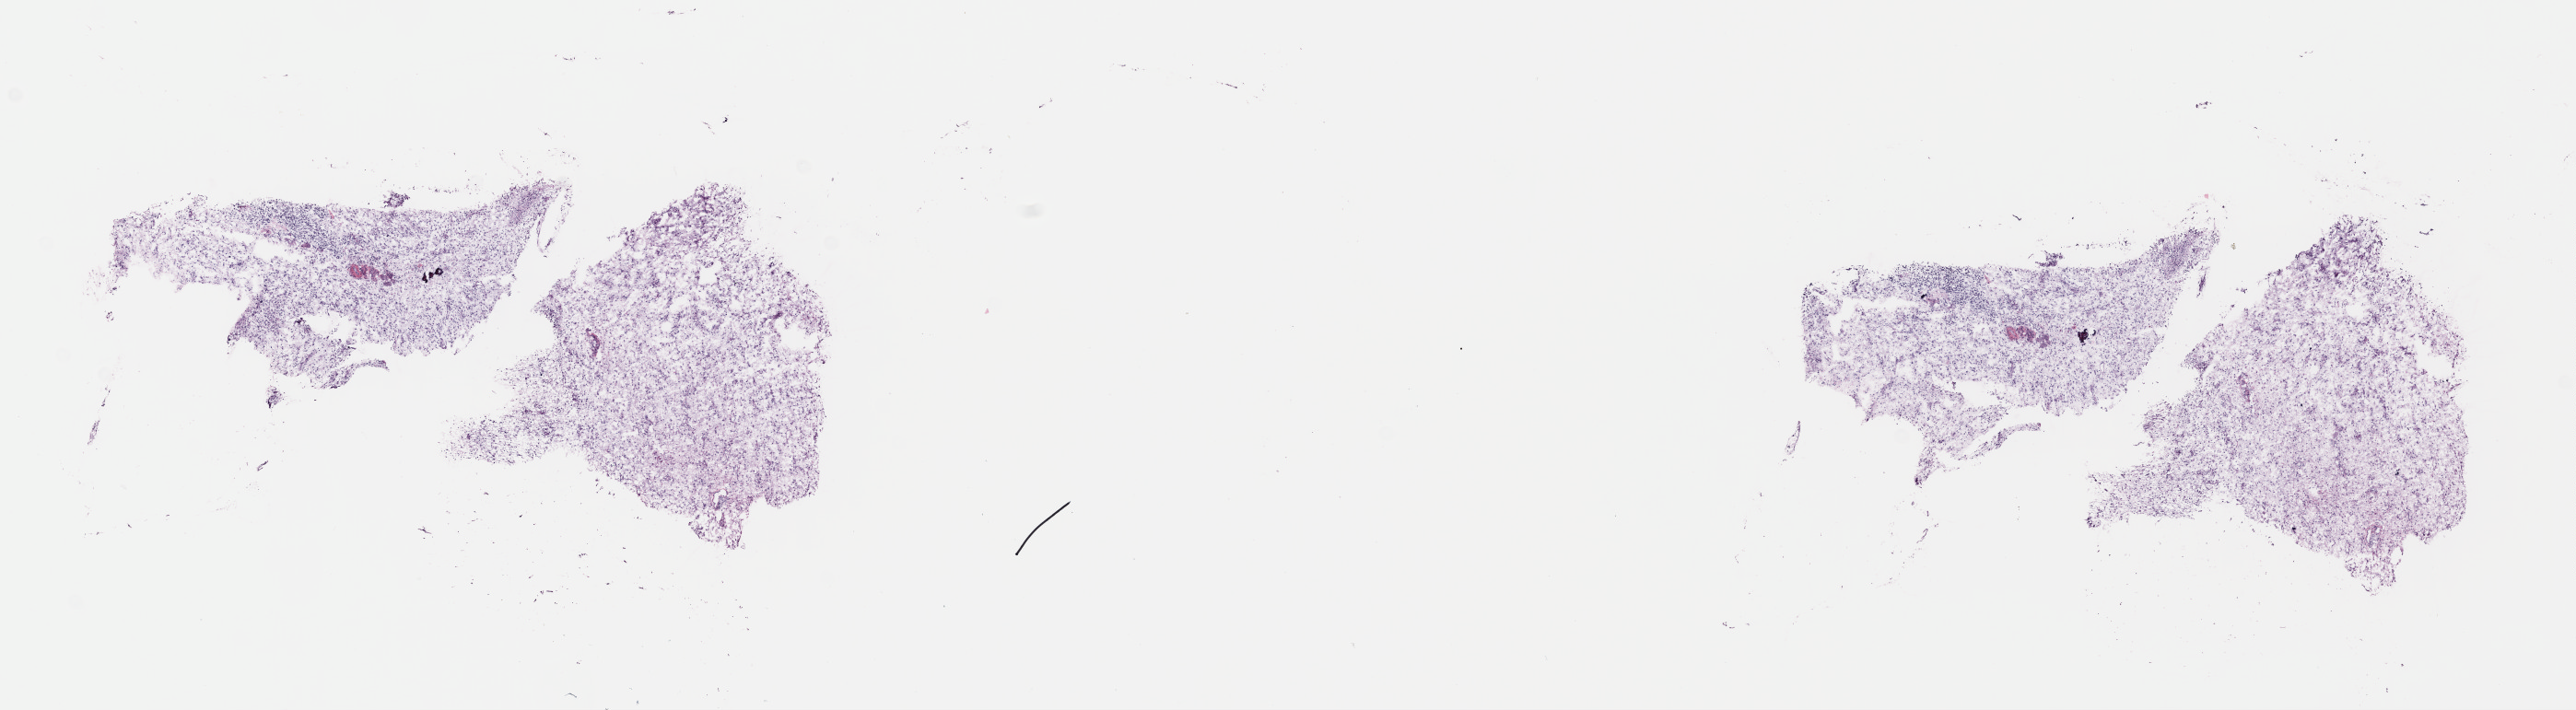
Whole-slide histology image, H&E-stained — low-resolution overview of the scanned area, about 22.0 x 6.1 mm (acquisition: 40x scan); frozen section from the top of the tissue portion; sample: primary tumour, brain. Female, age 39 years at initial diagnosis. Histologic grade: G2 (moderately differentiated). Composition of this section per pathologist review: tumour cells 40%, tumour nuclei 80%, normal cells 10%, stromal cells 50%, necrosis 0%. Infiltration values recorded for this section: lymphocyte infiltration 0%, monocyte infiltration 0%, neutrophil infiltration 0%.
Histologic diagnosis: Astrocytoma, NOS. Laterality: left.